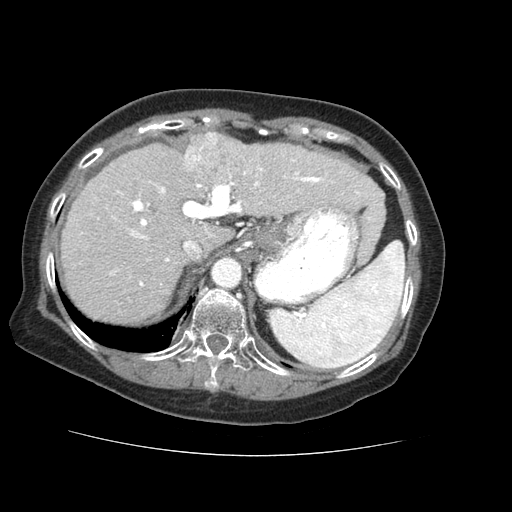
Contrast-enhanced abdominal CT (liver protocol), one axial slice; slice 46 of 73 in the series (ordered by position); reconstruction kernel STANDARD; soft-tissue window (W 400 / L 40 HU); 512 × 512 image matrix, field of view 360 × 360 mm. From the clinical record (not read from this slice): diagnosis: hepatocellular carcinoma (patient treated with transarterial chemoembolisation; whether this scan precedes or follows treatment is not stated here); TNM stage (as recorded): Stage-IVB; Child-Pugh class: A; tumour nodularity: uninodular.
Structures marked on this image (semi-automatic segmentation, software-assisted and operator-edited):
- liver parenchyma outside the tumour (the mass and vessels are separate outlines, so this box may not span the whole liver): bounding box (x1, y1, x2, y2) in pixels: (60, 132, 384, 322)
- mass: (183, 134, 243, 186)
- liver vessels: (110, 159, 370, 286)